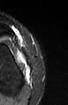
MRI of an extremity soft-tissue mass, one axial slice; slice 21 of 52 in the series (ordered by position); STIR; MR volume resampled by the dataset authors to the PET/CT grid (not the native acquisition matrix); 3.27 mm slice thickness; 68 × 105 image matrix, field of view 66 × 103 mm. Female patient. From the clinical record (not read from this slice): histological type: spindle cell suggestive of biphasic synovial sarcoma; grade: intermediate; site of the primary tumour: left knee.
Outlined on this slice (expert contour drawn on MRI and transferred to this co-registered scan by the dataset authors):
- gross tumour volume including surrounding oedema: bounding box <17,52,31,81> (left, top, right, bottom; pixels)
- gross tumour volume (mass): <17,52,31,80>